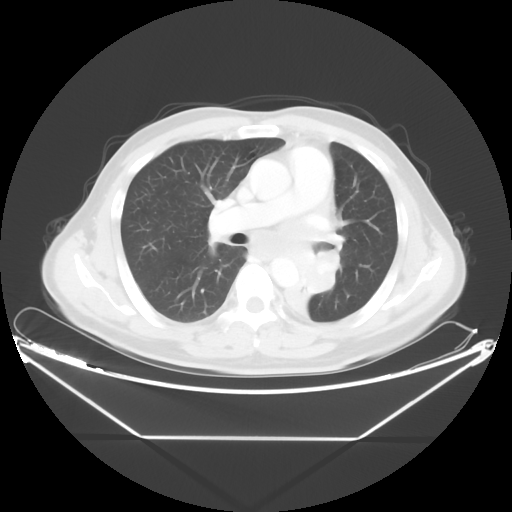
Chest CT, one axial slice. Position 27 of 48 along the scan axis. 120 kVp. Lung window (W 1500 / L -600 HU). 5 mm slice thickness. 512 × 512 image matrix. Male patient, age 58 years. Case-level facts recorded for this patient, not image findings: clinical TNM (as recorded): T3 N3 M0.
Structures marked on this image (bounding box drawn by a radiologist):
- lung tumour (recorded histology: squamous cell carcinoma): bounding box (x1, y1, x2, y2) in pixels: (280, 247, 337, 327)